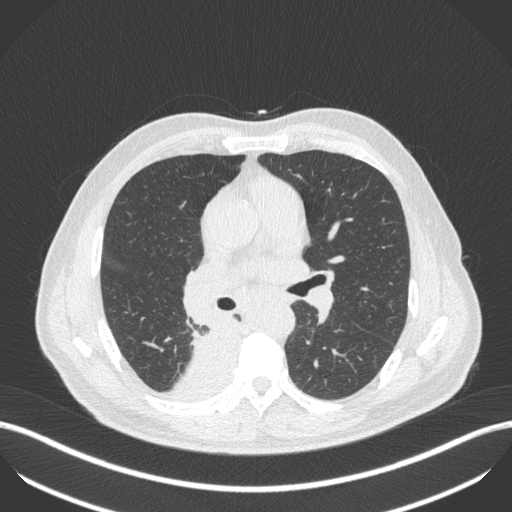
Chest CT, one axial slice; reconstruction kernel B31f; 100 kVp; lung window (W 1500 / L -600 HU); 512 × 512 image matrix, field of view 400 × 400 mm. Patient: male, 61 years. From the clinical record (not read from this slice): clinical TNM (as recorded): T1 N0 M0.
Annotated regions visible in this slice (rectangle marked by the reading radiologist):
- lung tumour (recorded histology: small cell carcinoma): bounding box (x1, y1, x2, y2) in pixels: (186, 314, 244, 370)